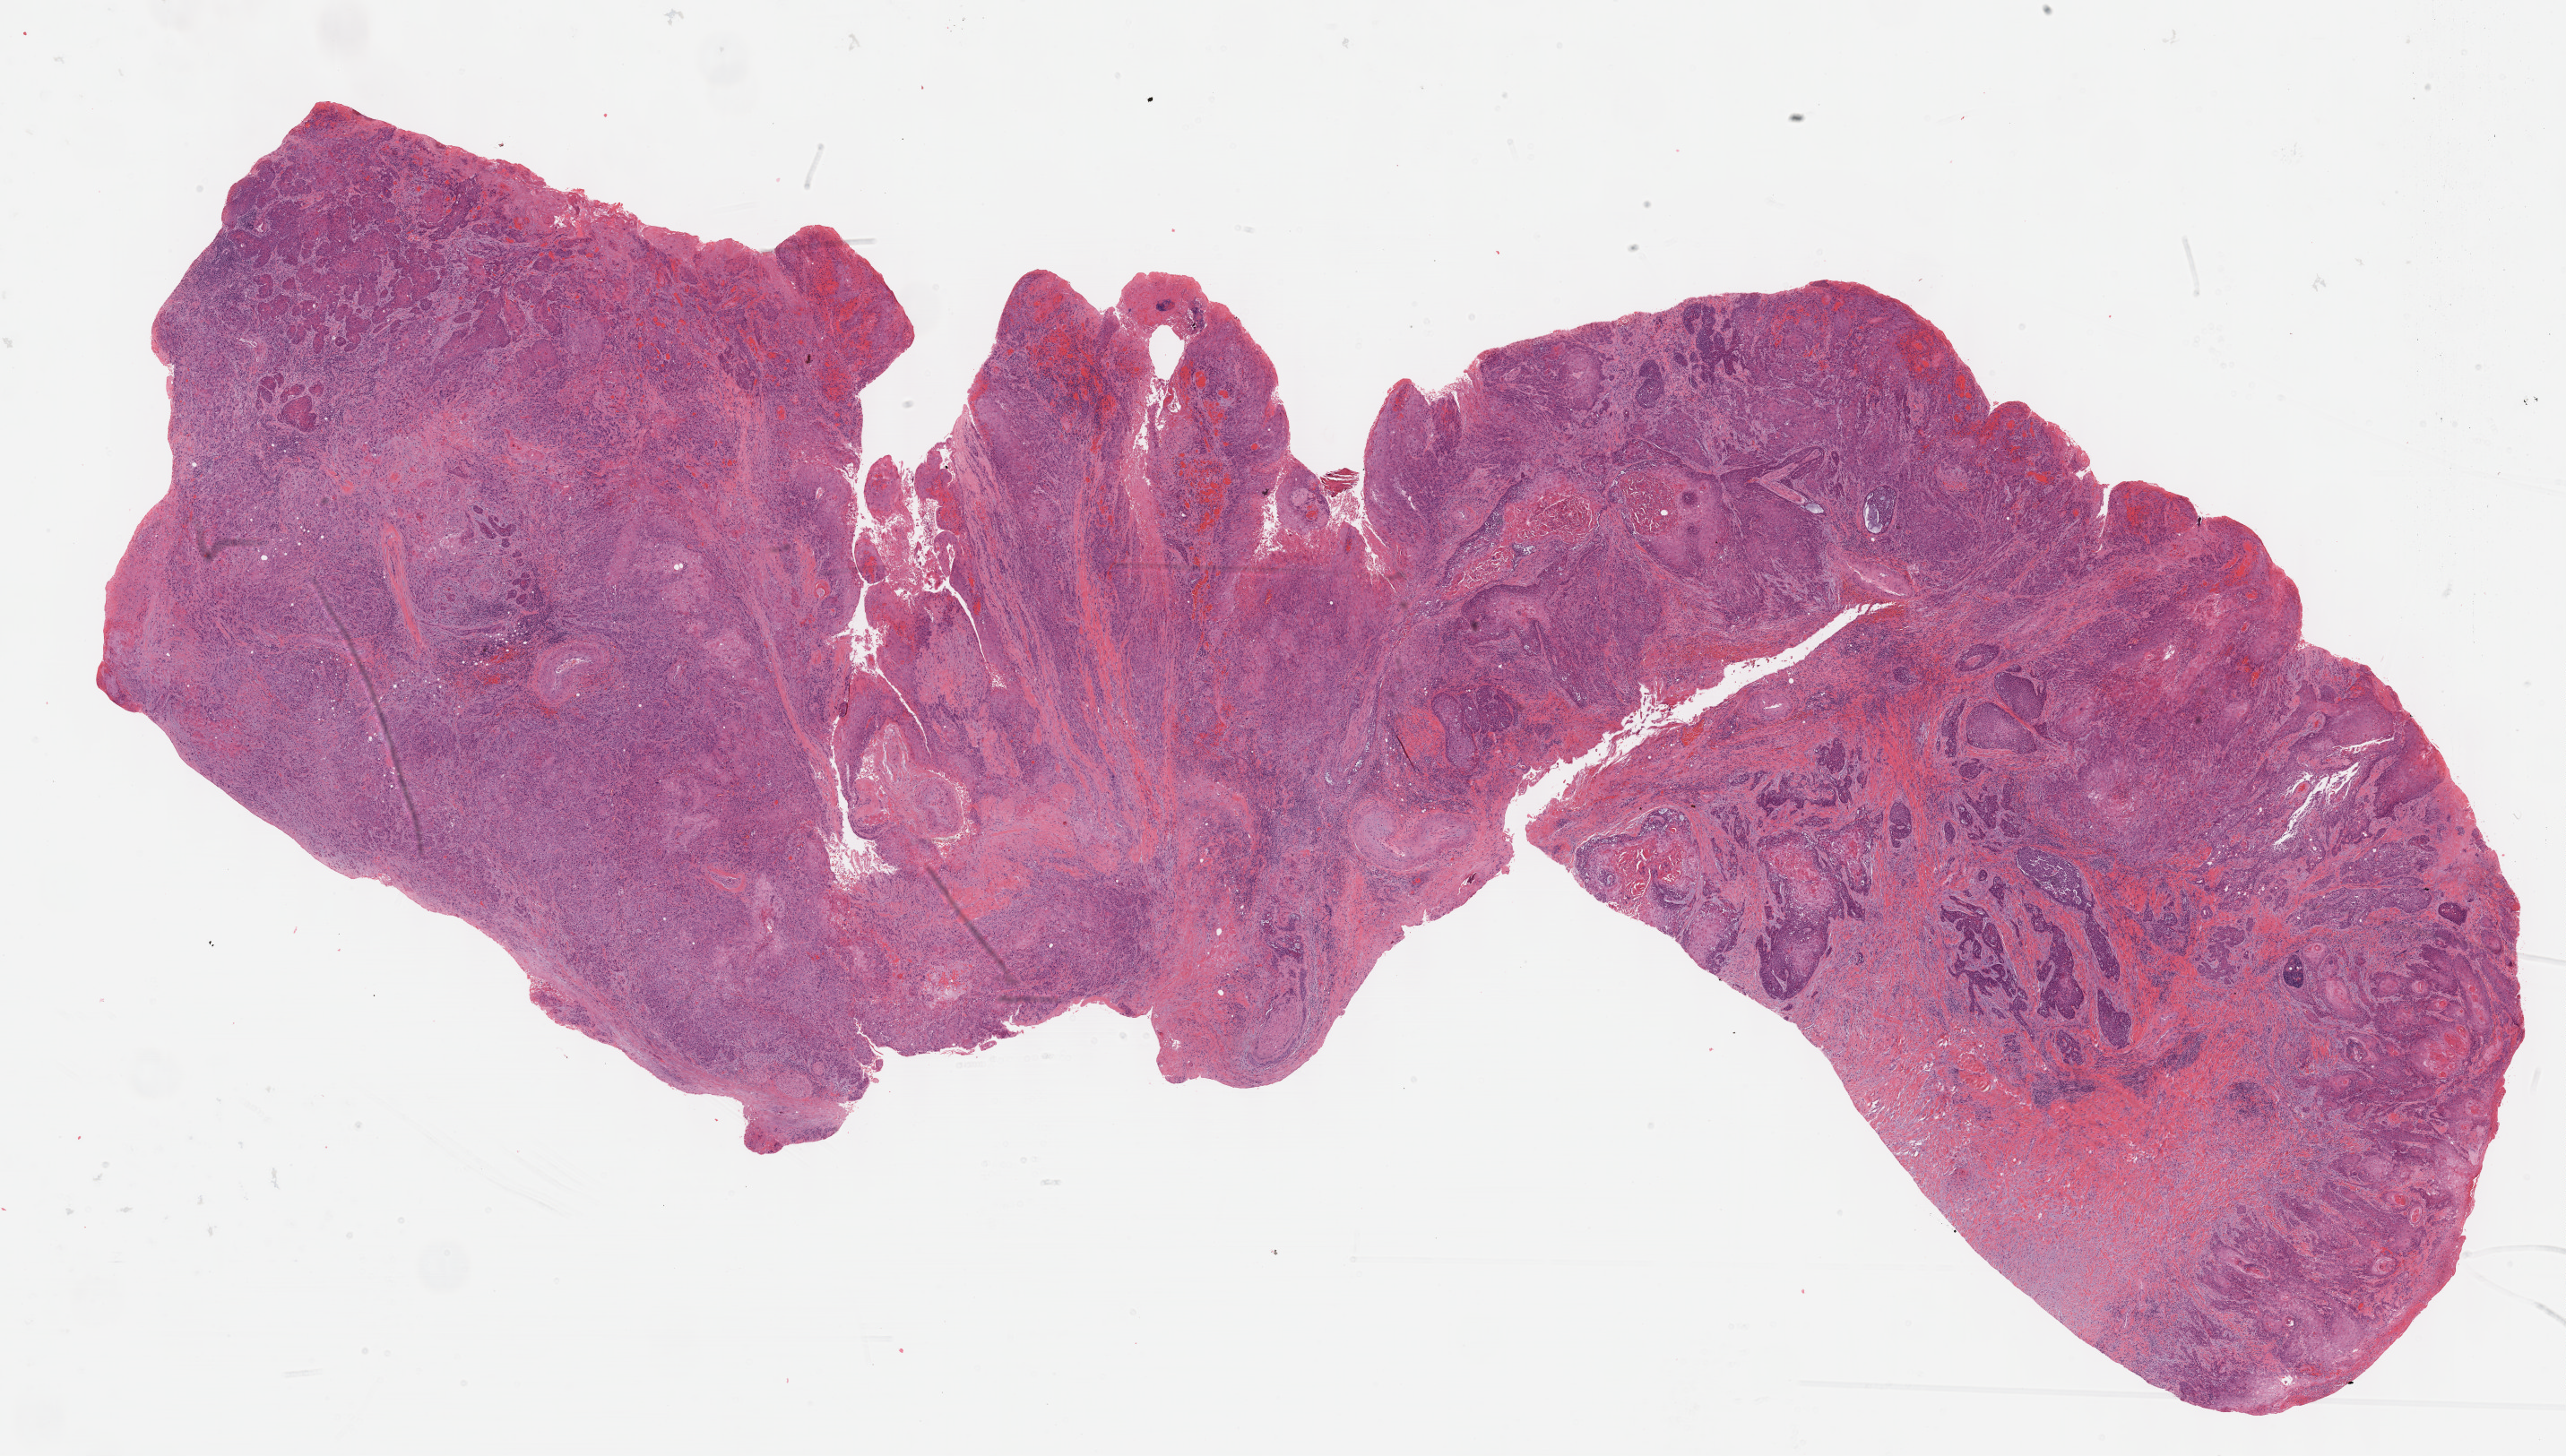
H&E-stained whole-slide image — whole scanned area (about 23.1 x 13.1 mm) shown as a low-resolution overview, FFPE section, primary tumour sample from the head and neck. Patient: female, age at initial diagnosis 85 years. Histologic grade: G2 (moderately differentiated).
• TNM: T2 NX
• pathologic diagnosis: Squamous cell carcinoma, NOS
• AJCC pathologic stage: II (7th edition)